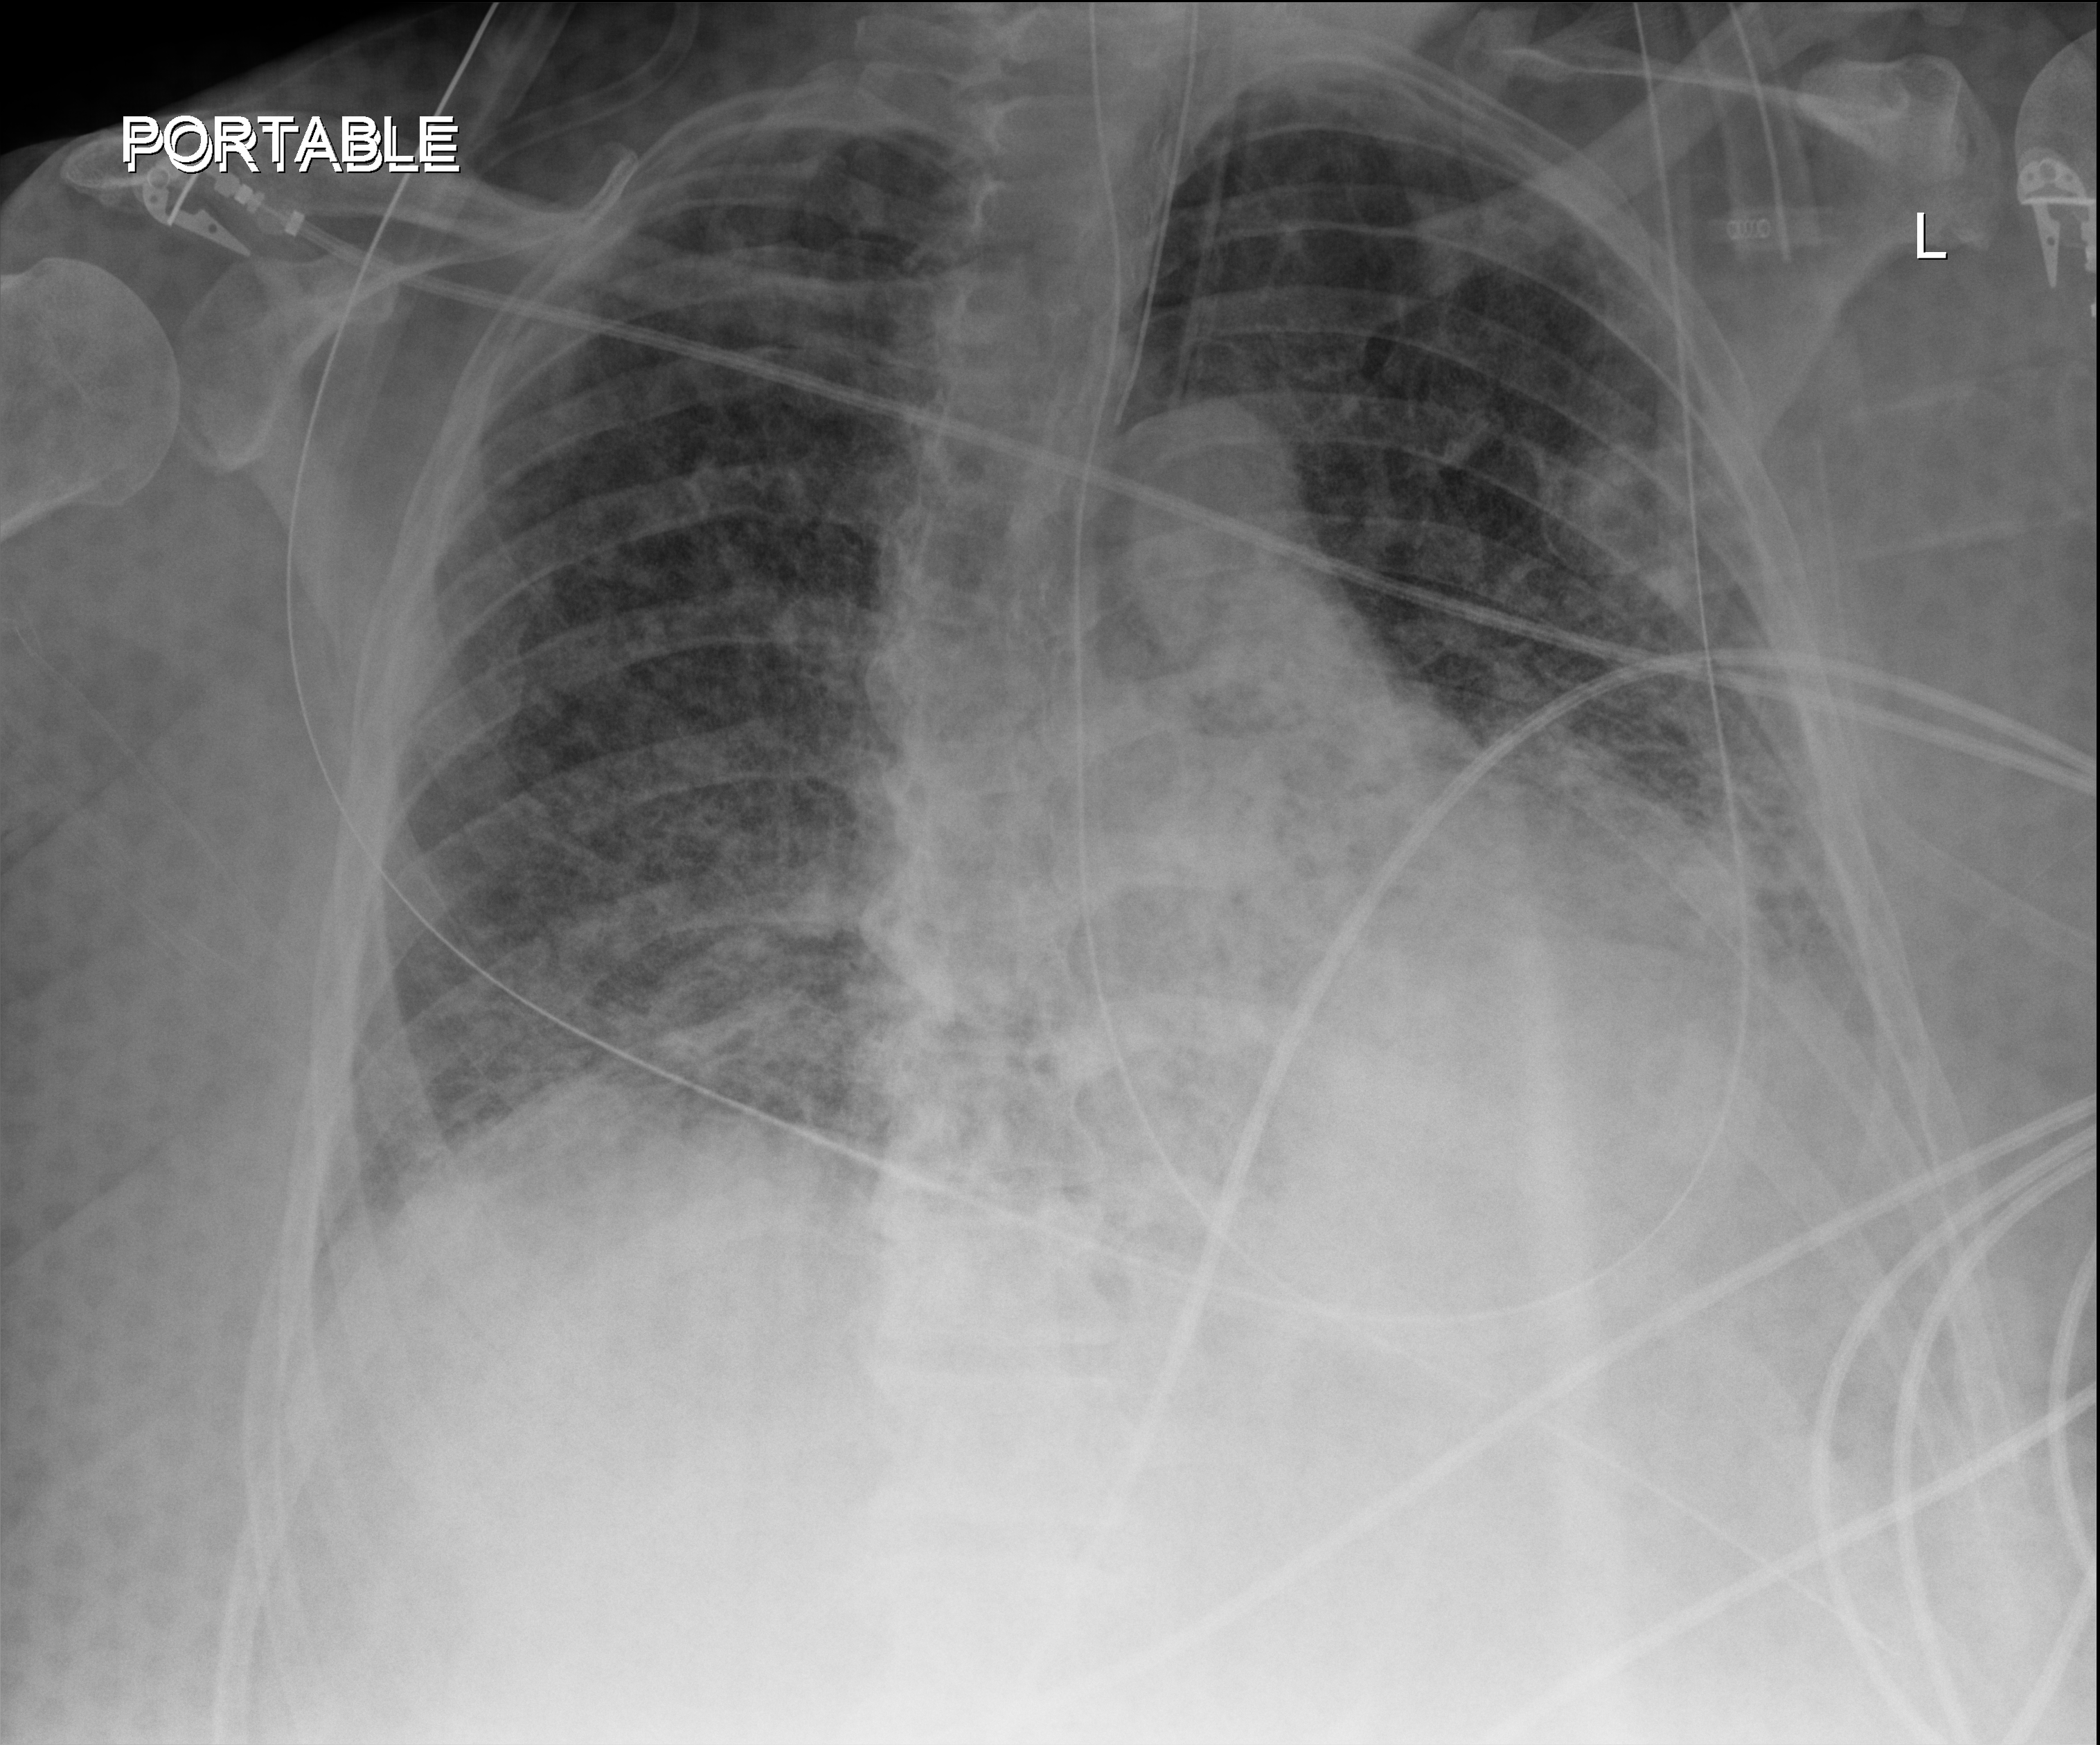
Chest X-ray (portable); anteroposterior (AP) projection. Adult patient hospitalised with COVID-19, age 18–59 years.
From the hospital-stay record, not from the radiograph (when in the stay this image was taken is not recorded):
- admitted to intensive care during this hospital stay: yes
- mechanically ventilated during this hospital stay: yes